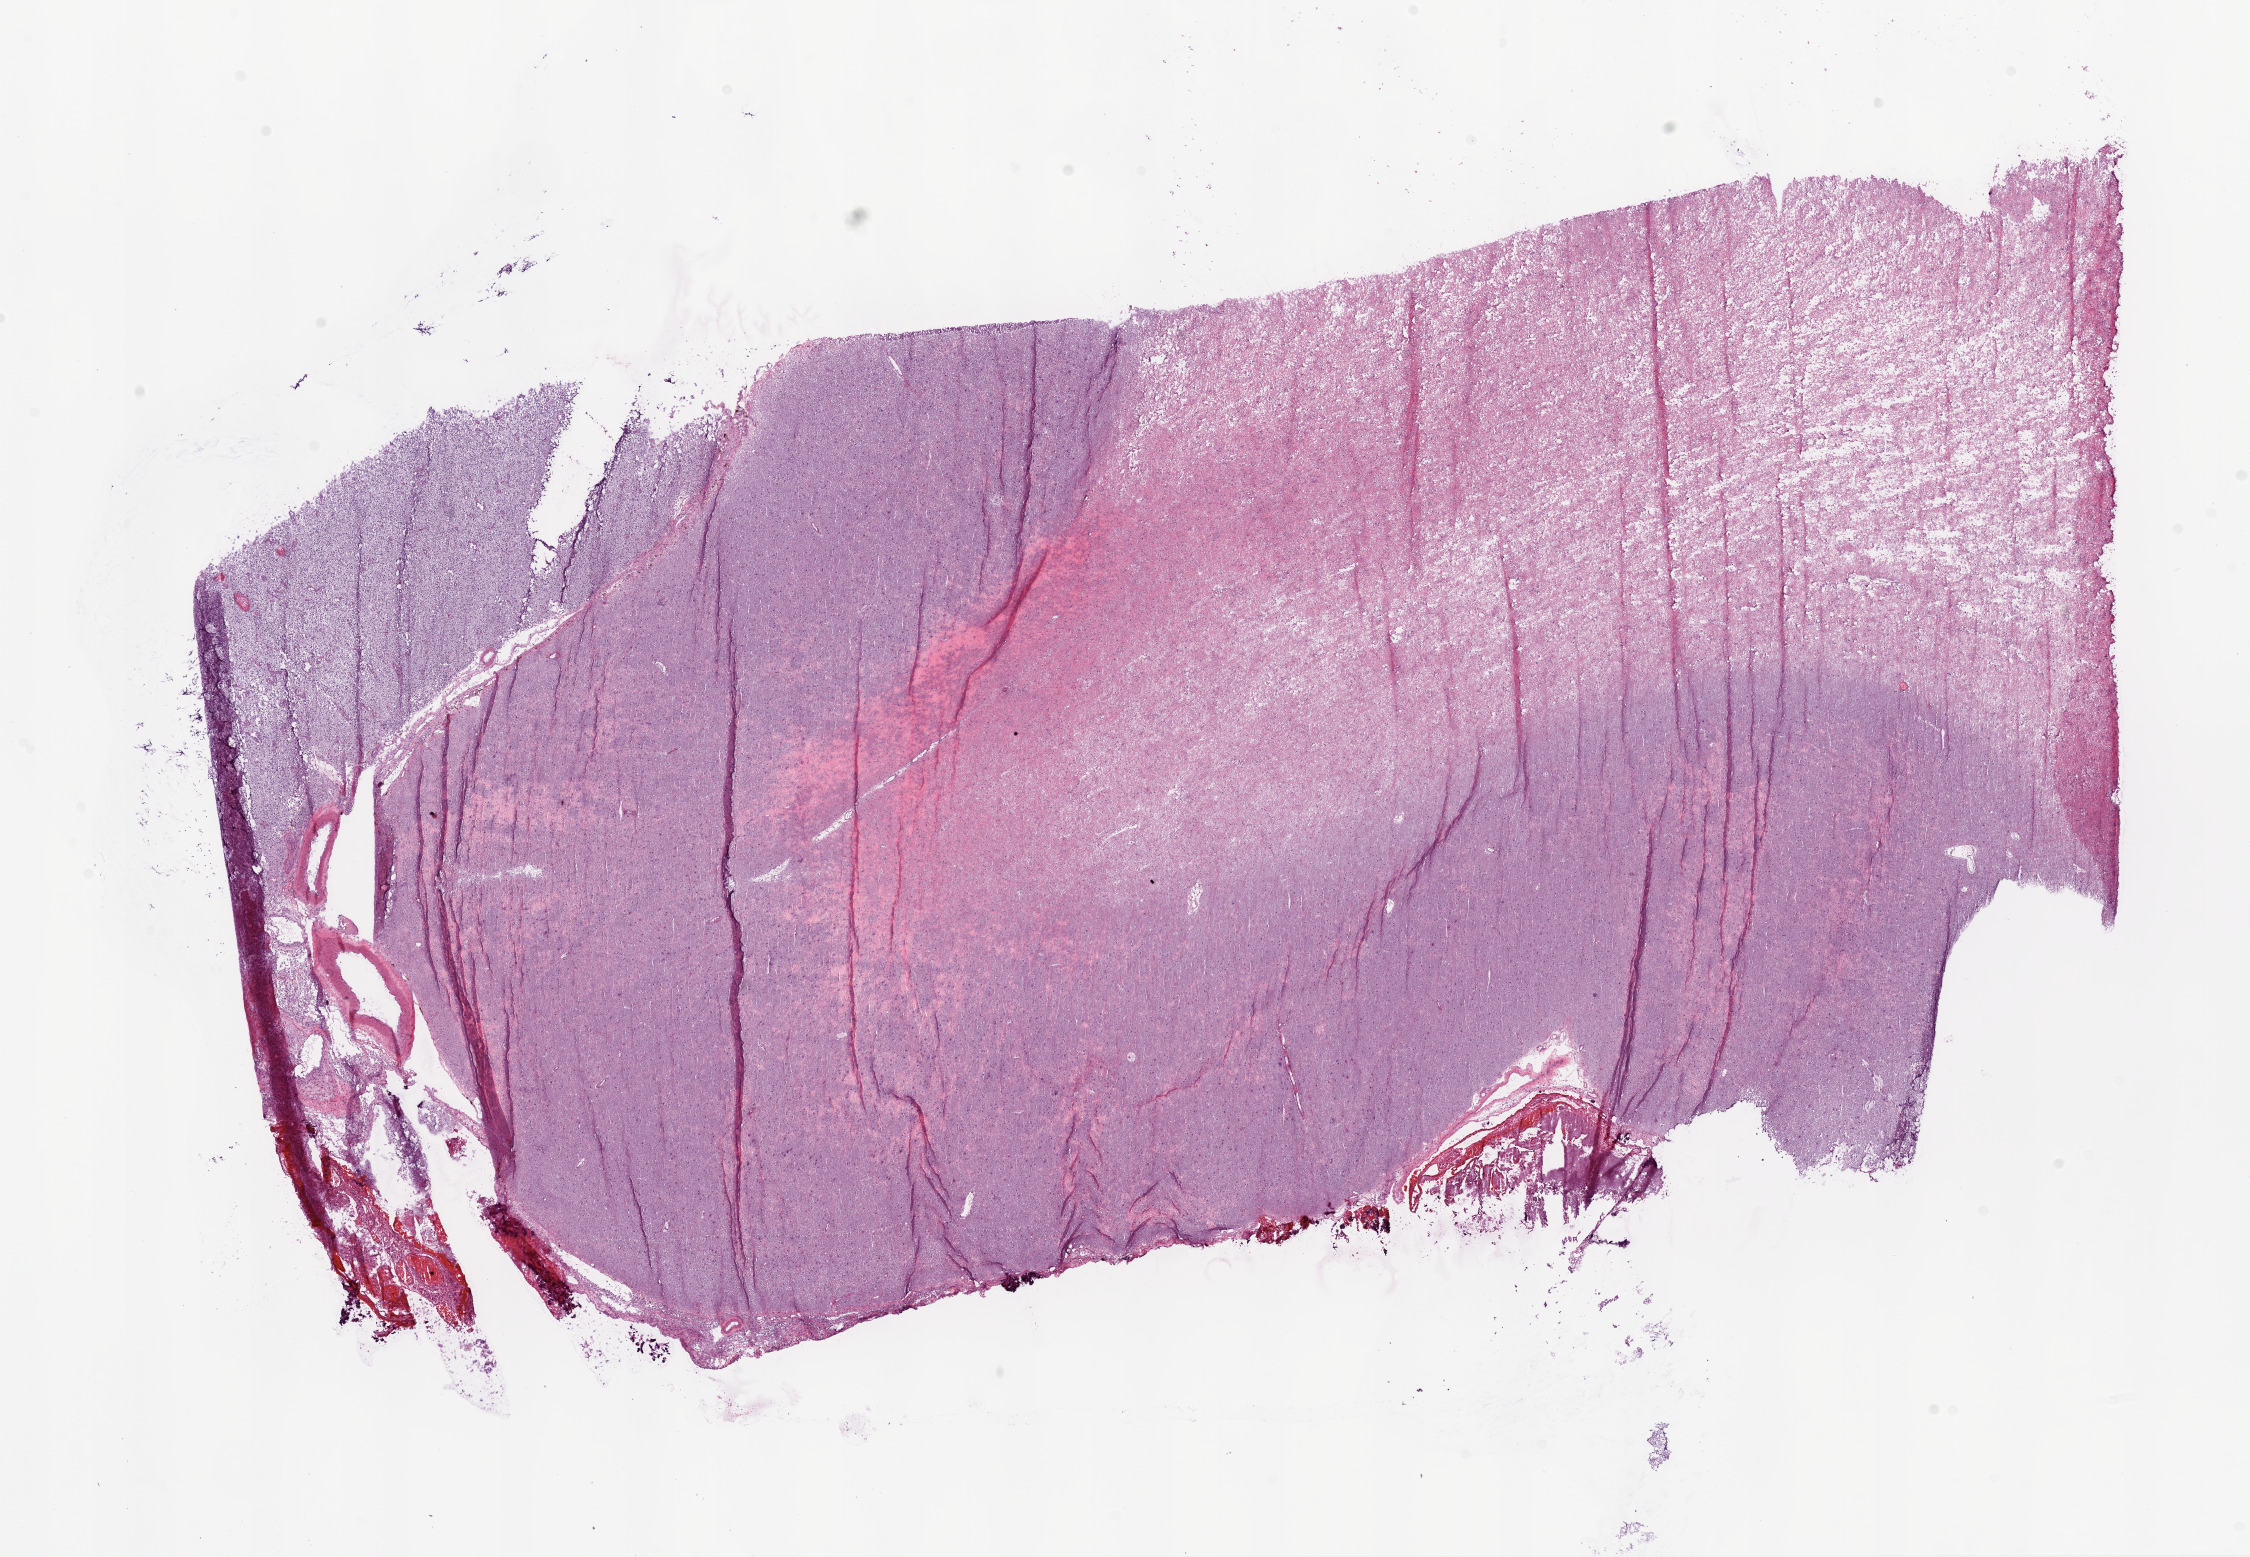
H&E-stained whole-slide image, low-resolution overview of the scanned area, about 18.1 x 12.5 mm (from a 20x scan). Composition of this section per pathologist review: tumour cells 40%, tumour nuclei 10%, normal cells 60%, stromal cells 0%, necrosis 0%.
• specimen: frozen section from the bottom of the tissue portion; brain, primary tumour sample